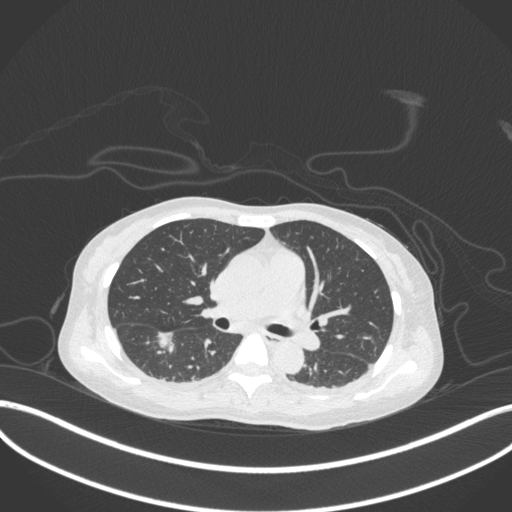
Chest CT, one axial slice. Slice 180 of 260 in the series (ordered by position). Reconstruction kernel B31f. 120 kVp. Lung window (W 1500 / L -600 HU). 1 mm slice thickness. 512 × 512 image matrix, field of view 400 × 400 mm. Female patient, age 44 years. From the clinical record (not read from this slice): clinical TNM (as recorded): T1c N0 M0.
Structures marked on this image (rectangle marked by the reading radiologist):
- lung tumour (recorded histology: adenocarcinoma): bounding box [x1, y1, x2, y2] px = [155, 327, 178, 355]